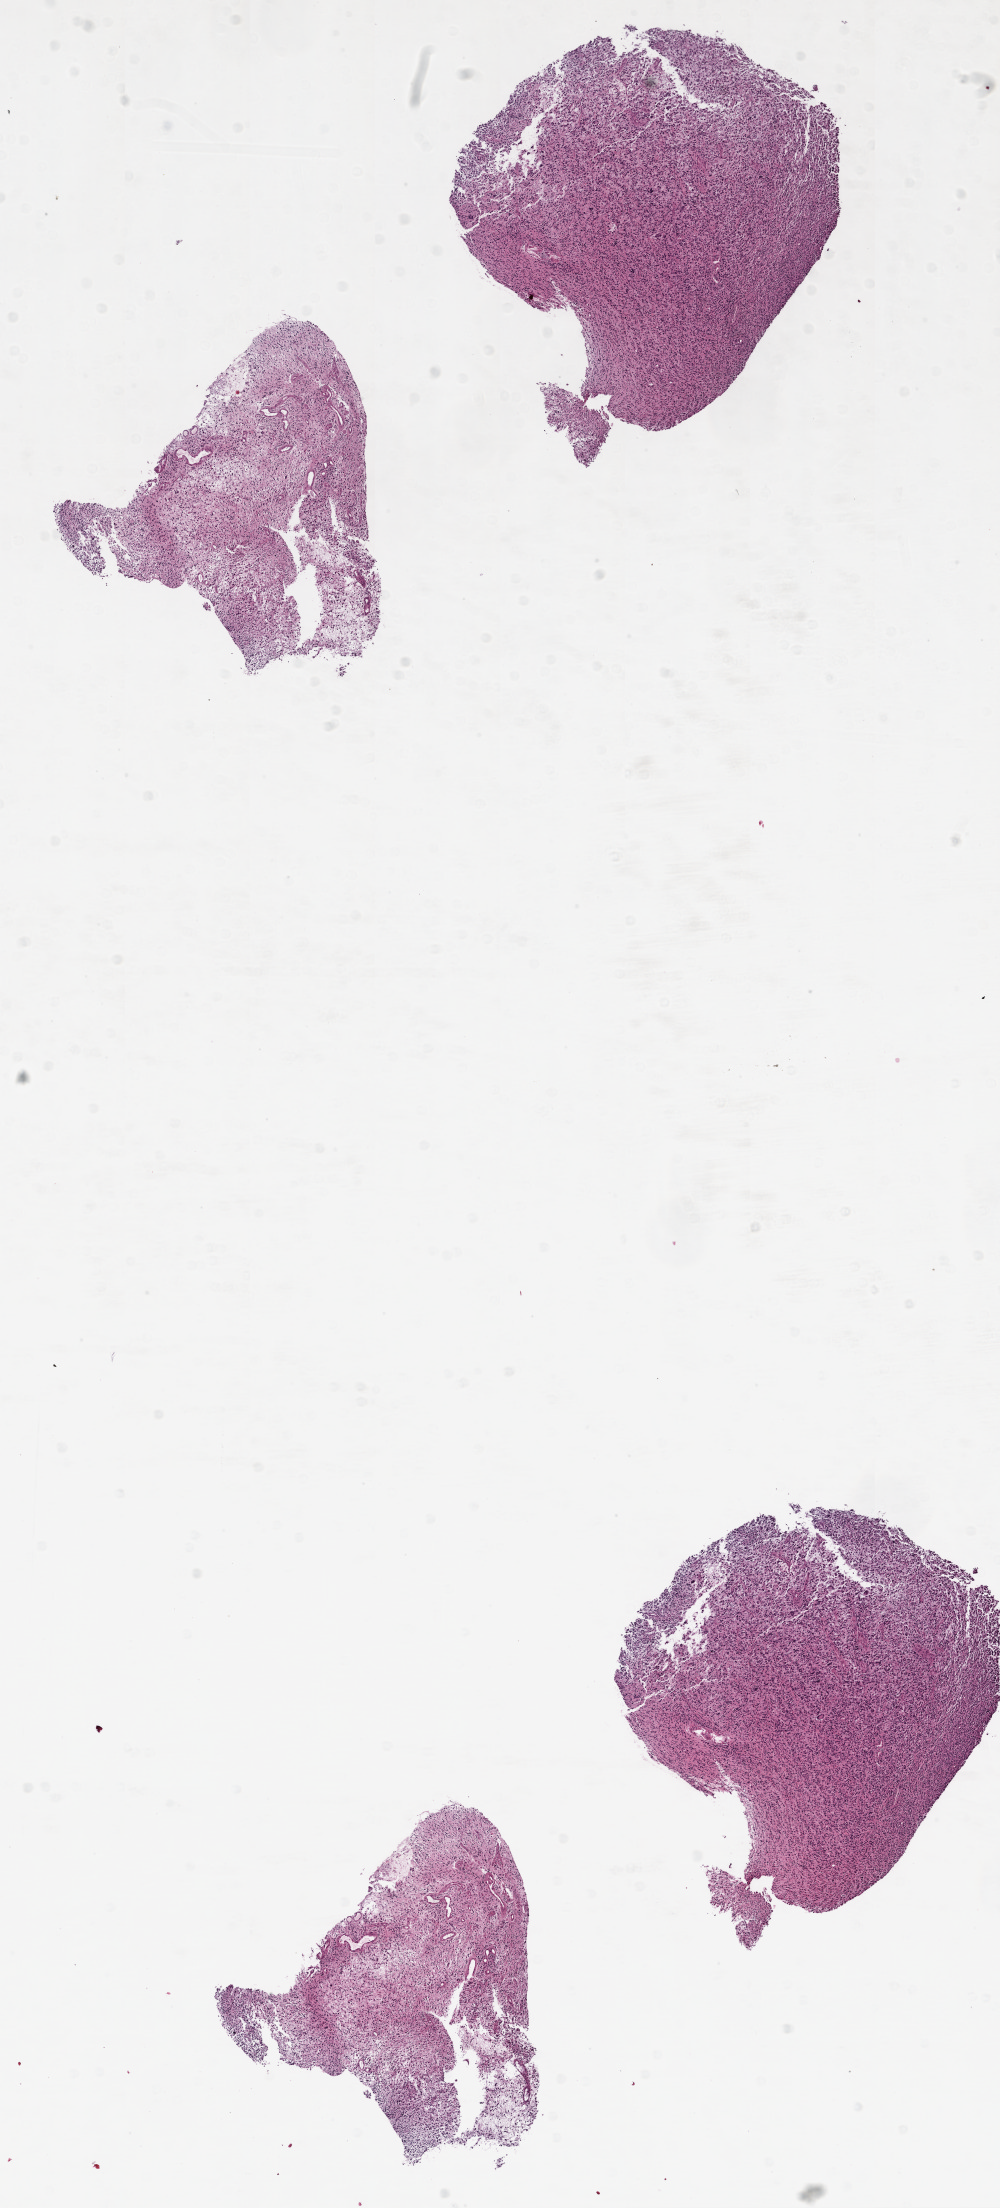
H&E whole-slide image — low-resolution overview of the scanned area, about 8.0 x 17.7 mm, formalin-fixed paraffin-embedded (FFPE) diagnostic section, primary tumour sample from the brain. Male, age 69 years at initial diagnosis.
Pathologic diagnosis: Glioblastoma.